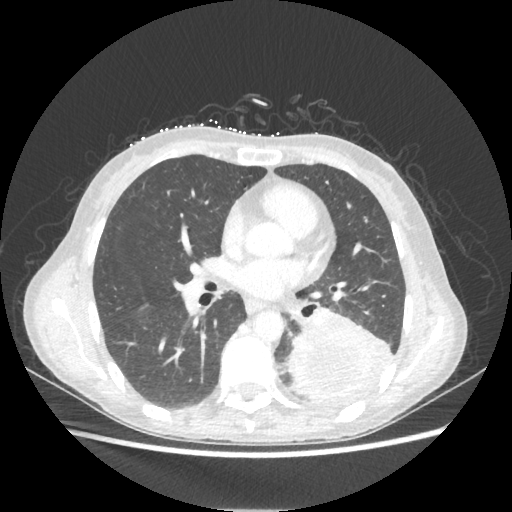
Chest CT, one axial slice; slice 113 of 221 in the series (ordered by position); reconstruction kernel STANDARD; lung window (W 1500 / L -600 HU); 1.25 mm slice thickness; 512 × 512 image matrix, field of view 360 × 360 mm. Female patient, age 53 years. From the clinical record (not read from this slice): clinical TNM (as recorded): T3 N0 M0.
Annotated regions visible in this slice (rectangle marked by the reading radiologist):
- lung tumour (recorded histology: adenocarcinoma): bounding box [x1, y1, x2, y2] px = [287, 310, 397, 407]